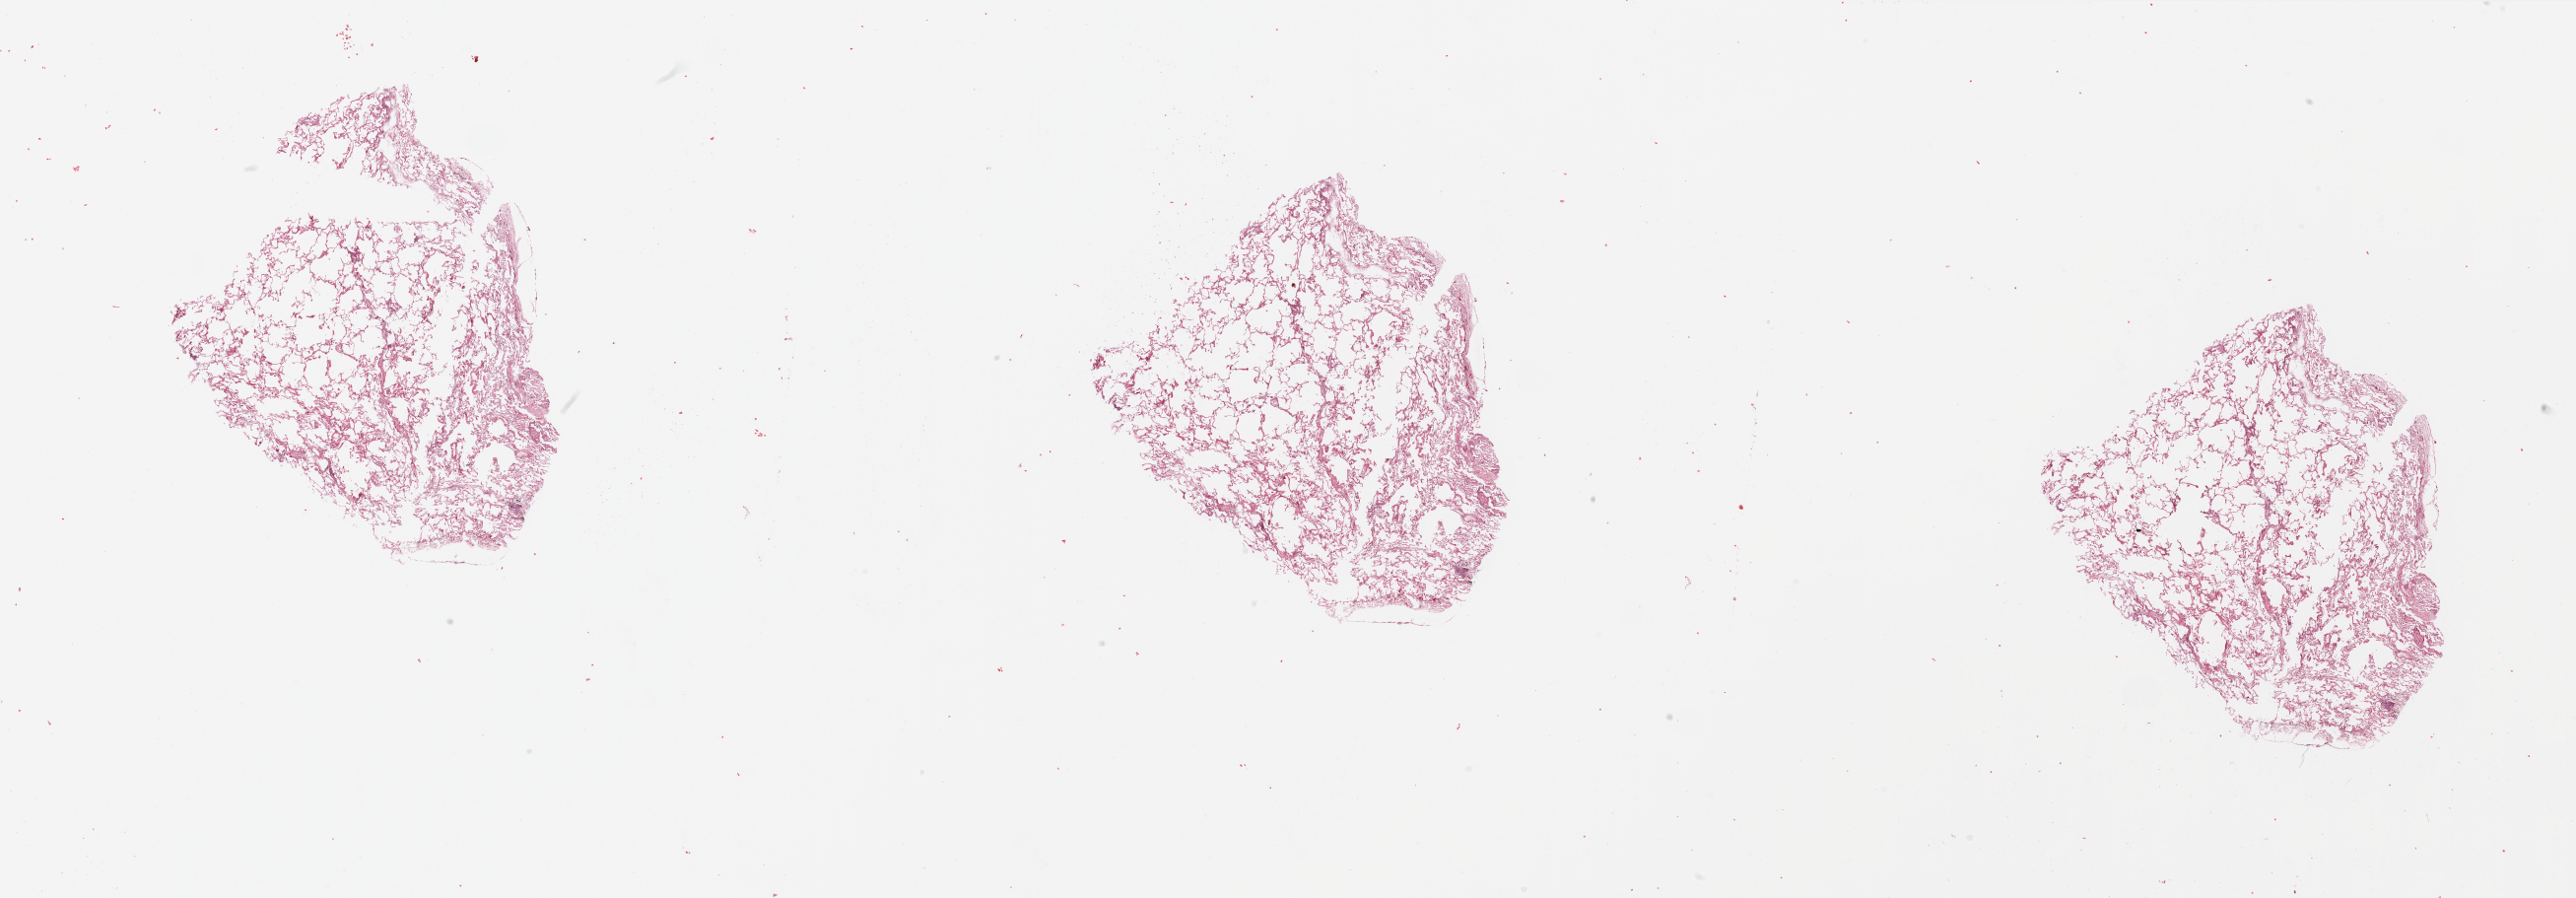
H&E-stained whole-slide image, low-resolution overview of the scanned area, about 41.3 x 14.4 mm (slide scanned at 20x), normal (non-tumour) tissue sample, sampled site: lung. 60-year-old female patient.
This section: normal (non-tumour) tissue from the same patient. Patient diagnosis: Adenocarcinoma, NOS.